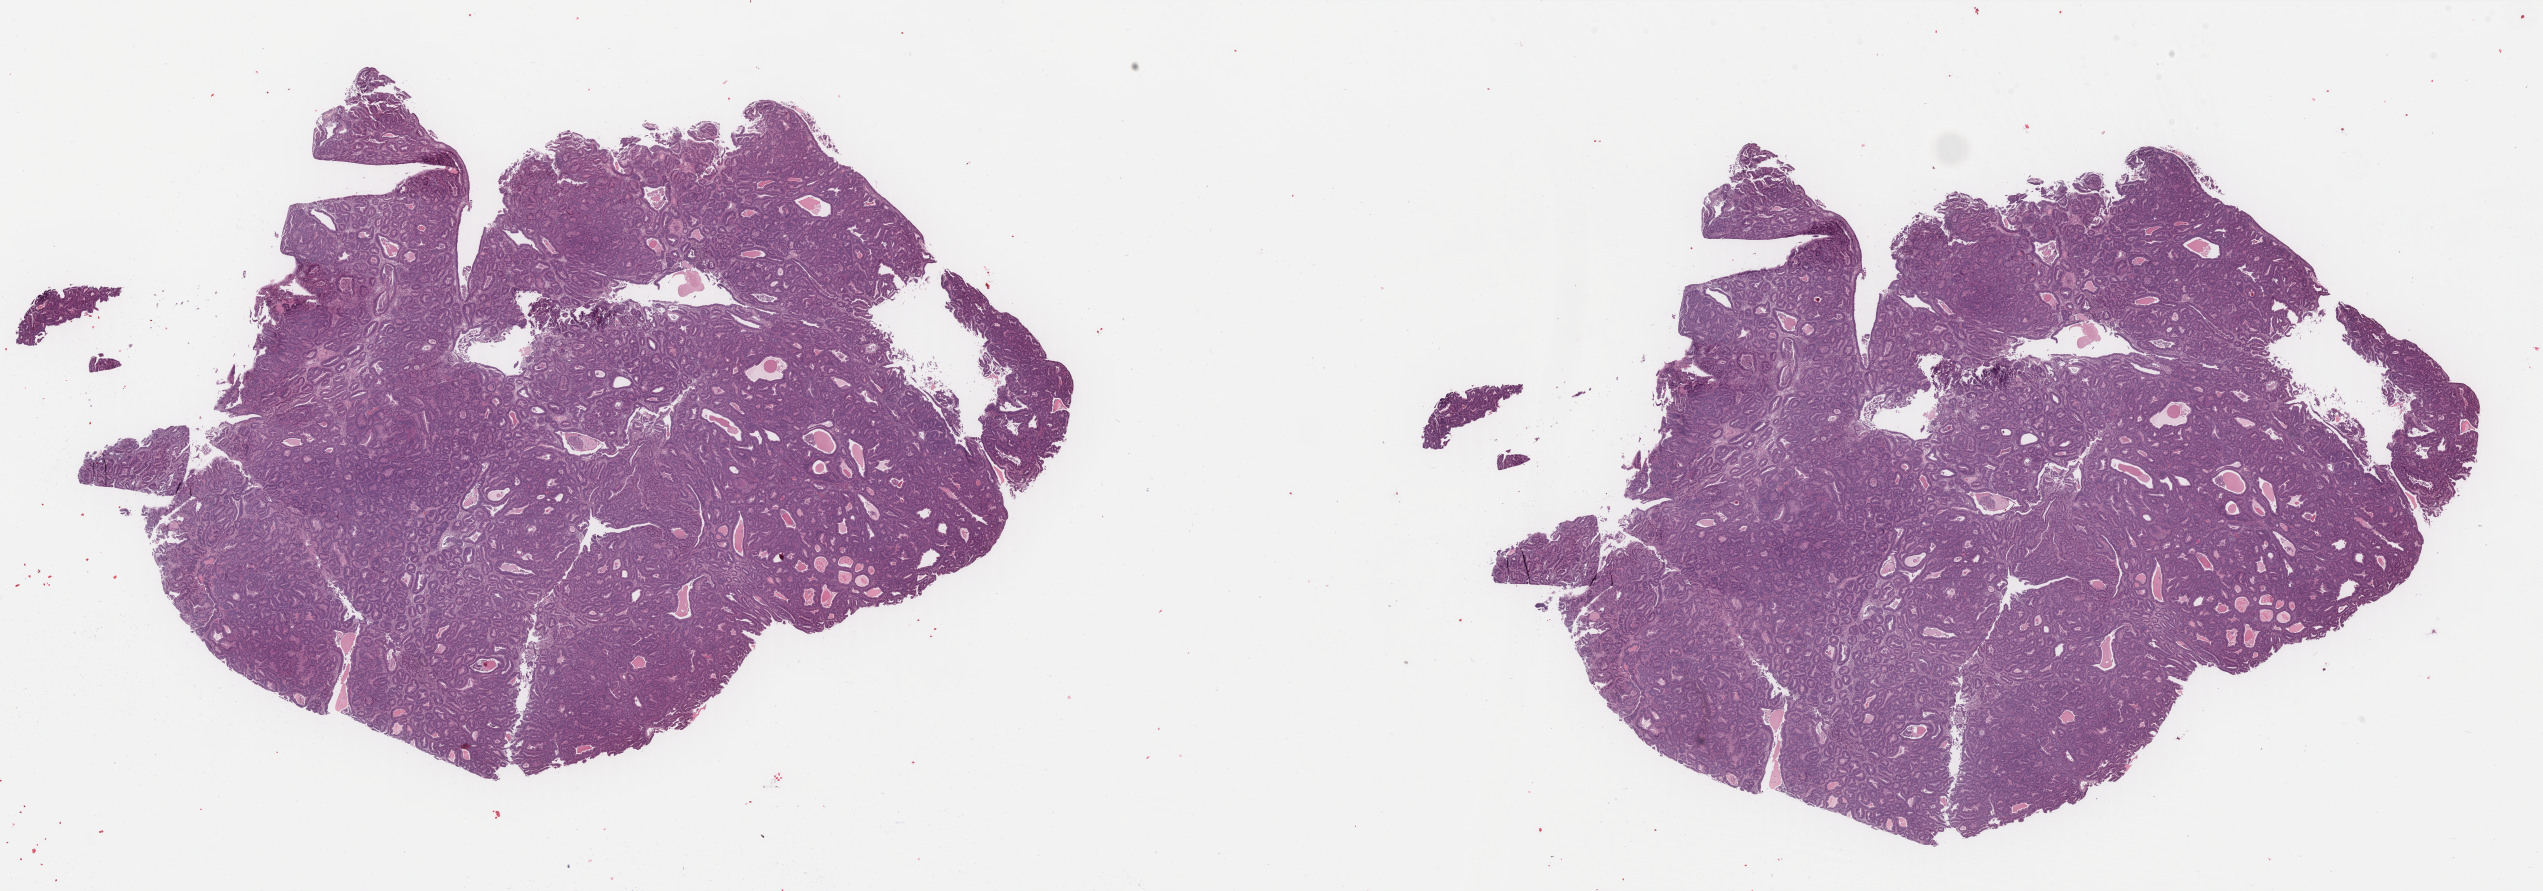
H&E-stained whole-slide image — a low-resolution overview of the entire scanned area, about 40.2 x 14.1 mm (slide scanned at 40x). Formalin-fixed paraffin-embedded (FFPE) diagnostic section. Primary tumour sample from the uterus. Female patient; age at initial diagnosis 83 years. Histologic grade: G1 (well differentiated).
Histologic diagnosis: Endometrioid adenocarcinoma, NOS (endometrium). FIGO stage: IA.